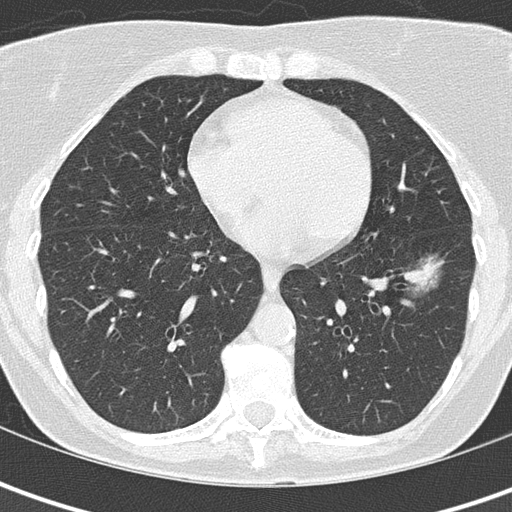
Low-dose screening chest CT, one axial slice; position 60 of 149 along the scan axis; 120 kVp; lung window (W 1500 / L -600 HU); 2 mm slice thickness; 512 × 512 image matrix, field of view 280 × 280 mm.
Annotated regions visible in this slice (outlined manually by an expert reader):
- lesion 1 (tumor, lower lobe of left lung): box from (x=404, y=259) to (x=439, y=288) px